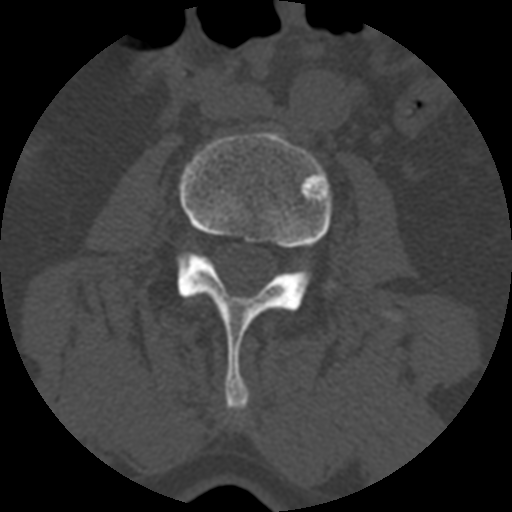
CT including the spine, one axial slice; position 306 of 399 along the scan axis; reconstruction kernel STANDARD; bone window (W 1800 / L 400 HU); 1.25 mm slice thickness; 512 × 512 image matrix. Patient age 71 years. From the clinical record (not read from this slice): primary cancer: prostate.
Annotated regions visible in this slice (semi-automatically segmented with operator editing):
- L2 vertebra: bounding box <192,294,197,298> (left, top, right, bottom; pixels)
- L3 vertebra: <177,131,403,412>